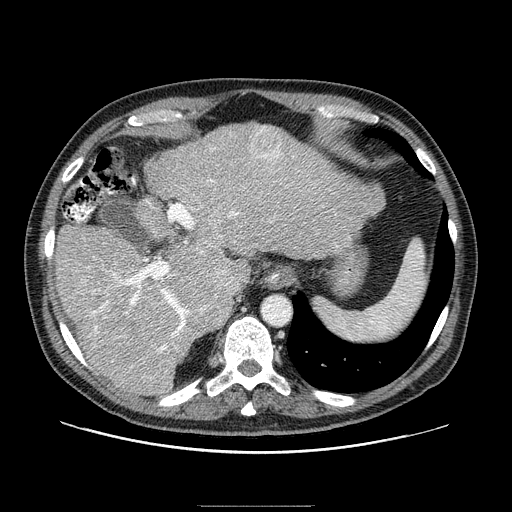
Contrast-enhanced abdominal CT (liver protocol), one axial slice; reconstruction kernel STANDARD; one of 2 acquisitions stored at this slice position; soft-tissue window (W 400 / L 40 HU); 2.5 mm slice thickness; 512 × 512 image matrix, field of view 400 × 400 mm. From the clinical record (not read from this slice): diagnosis: hepatocellular carcinoma (patient treated with transarterial chemoembolisation; whether this scan precedes or follows treatment is not stated here); TNM stage (as recorded): Stage-II; Child-Pugh class: A; tumour differentiation: well differentiated; tumour nodularity: multinodular.
Outlined on this slice (semi-automatic segmentation, software-assisted and operator-edited):
- abdominal aorta: bounding box <263,296,291,324> (left, top, right, bottom; pixels)
- liver parenchyma outside the tumour (the mass and vessels are separate outlines, so this box may not span the whole liver): <56,124,384,394>
- mass: <248,126,285,169>
- liver vessels: <87,148,338,367>